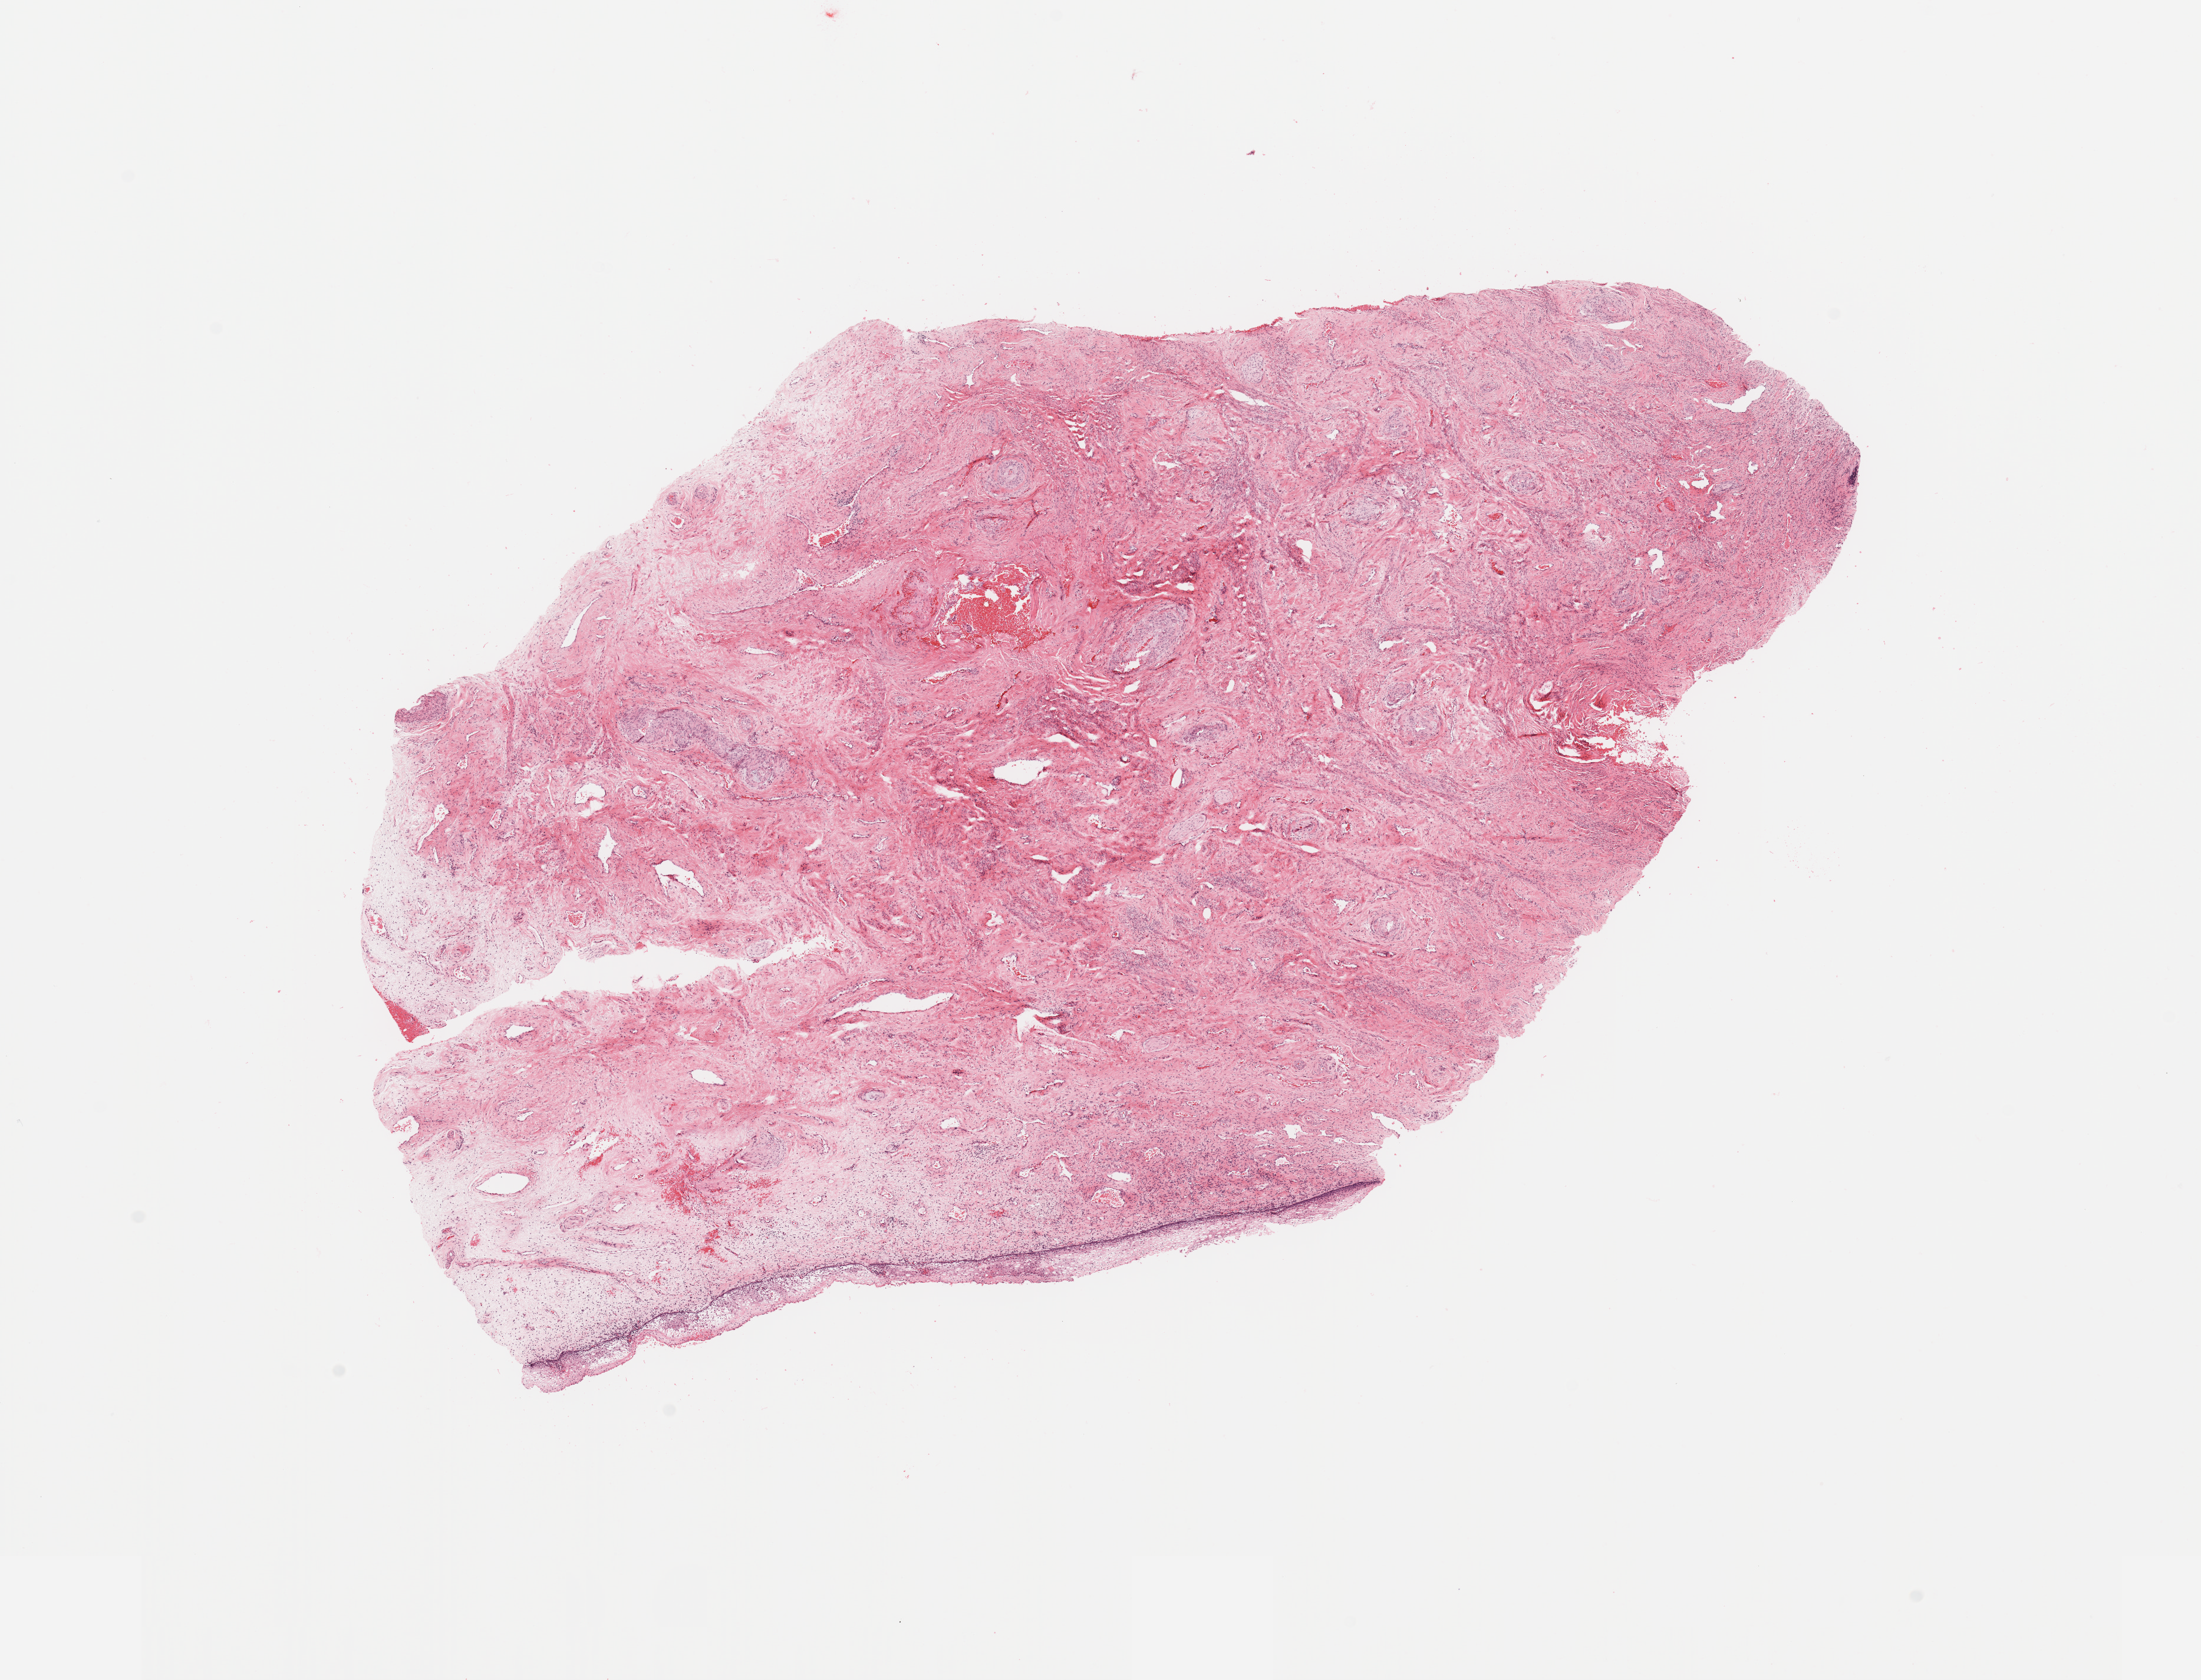
H&E-stained whole-slide image, shown as a low-resolution overview of the whole scanned area (about 14.8 x 11.3 mm); normal (non-tumour) tissue sample, sampled site: uterus. 60-year-old female patient.
This section: normal (non-tumour) tissue from the same patient. Patient diagnosis: Endometrioid adenocarcinoma, NOS.